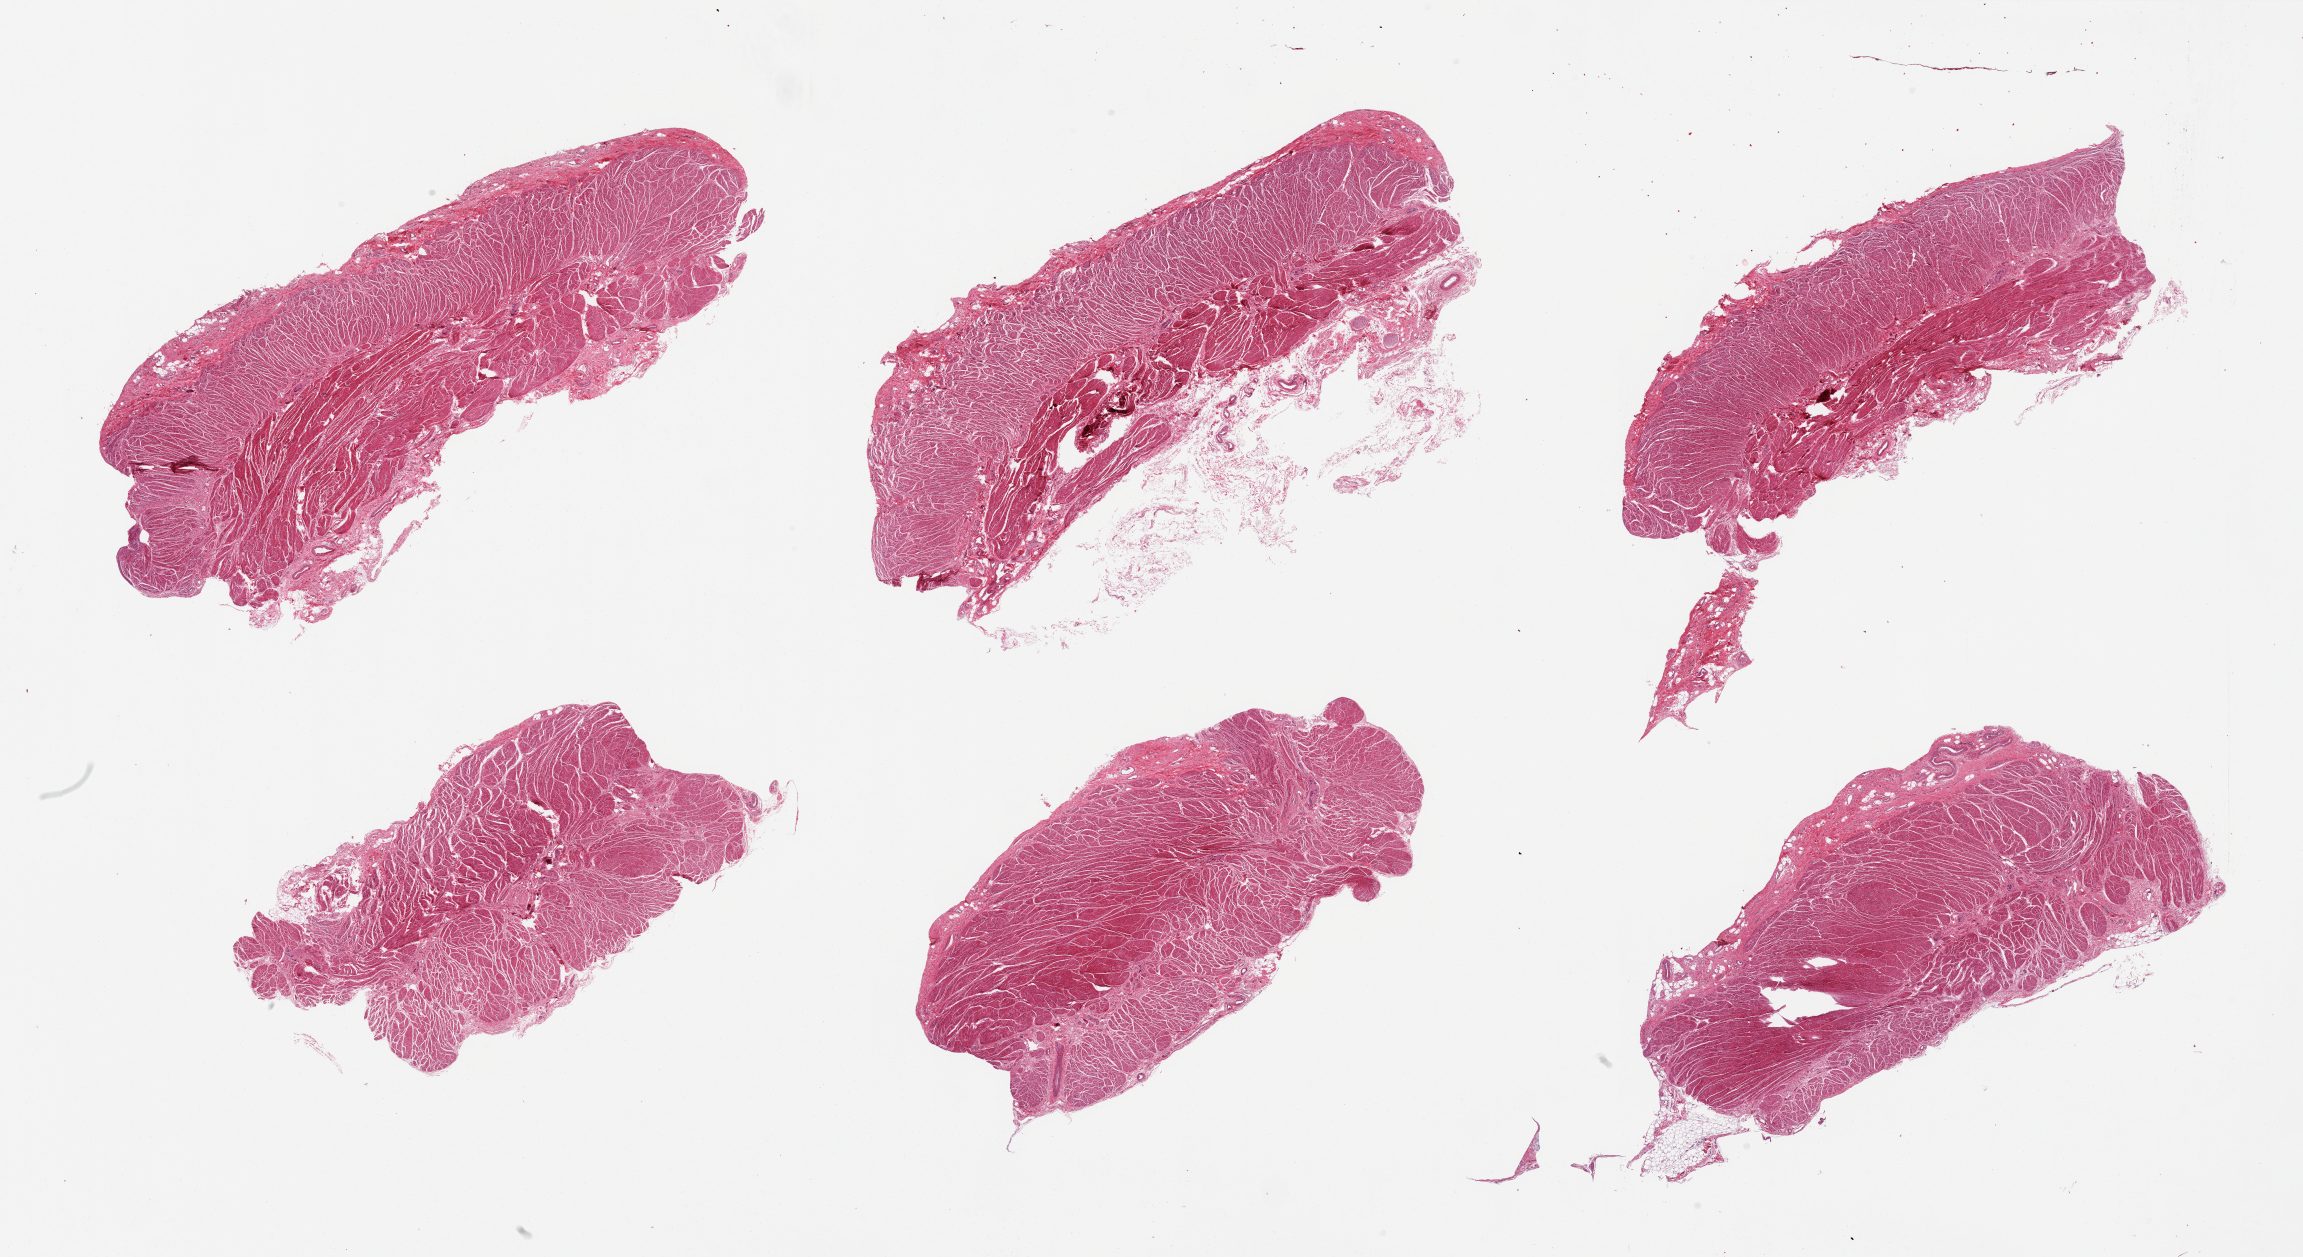
Whole-slide image, H&E stain, a low-resolution overview of the entire scanned area, about 36.4 x 19.9 mm (from a 20x scan). PAXgene-fixed, paraffin-embedded tissue. Target tissue: gastroesophageal junction. Donor tissue sample.
* review note (as recorded): 6 pieces, generally well dissected